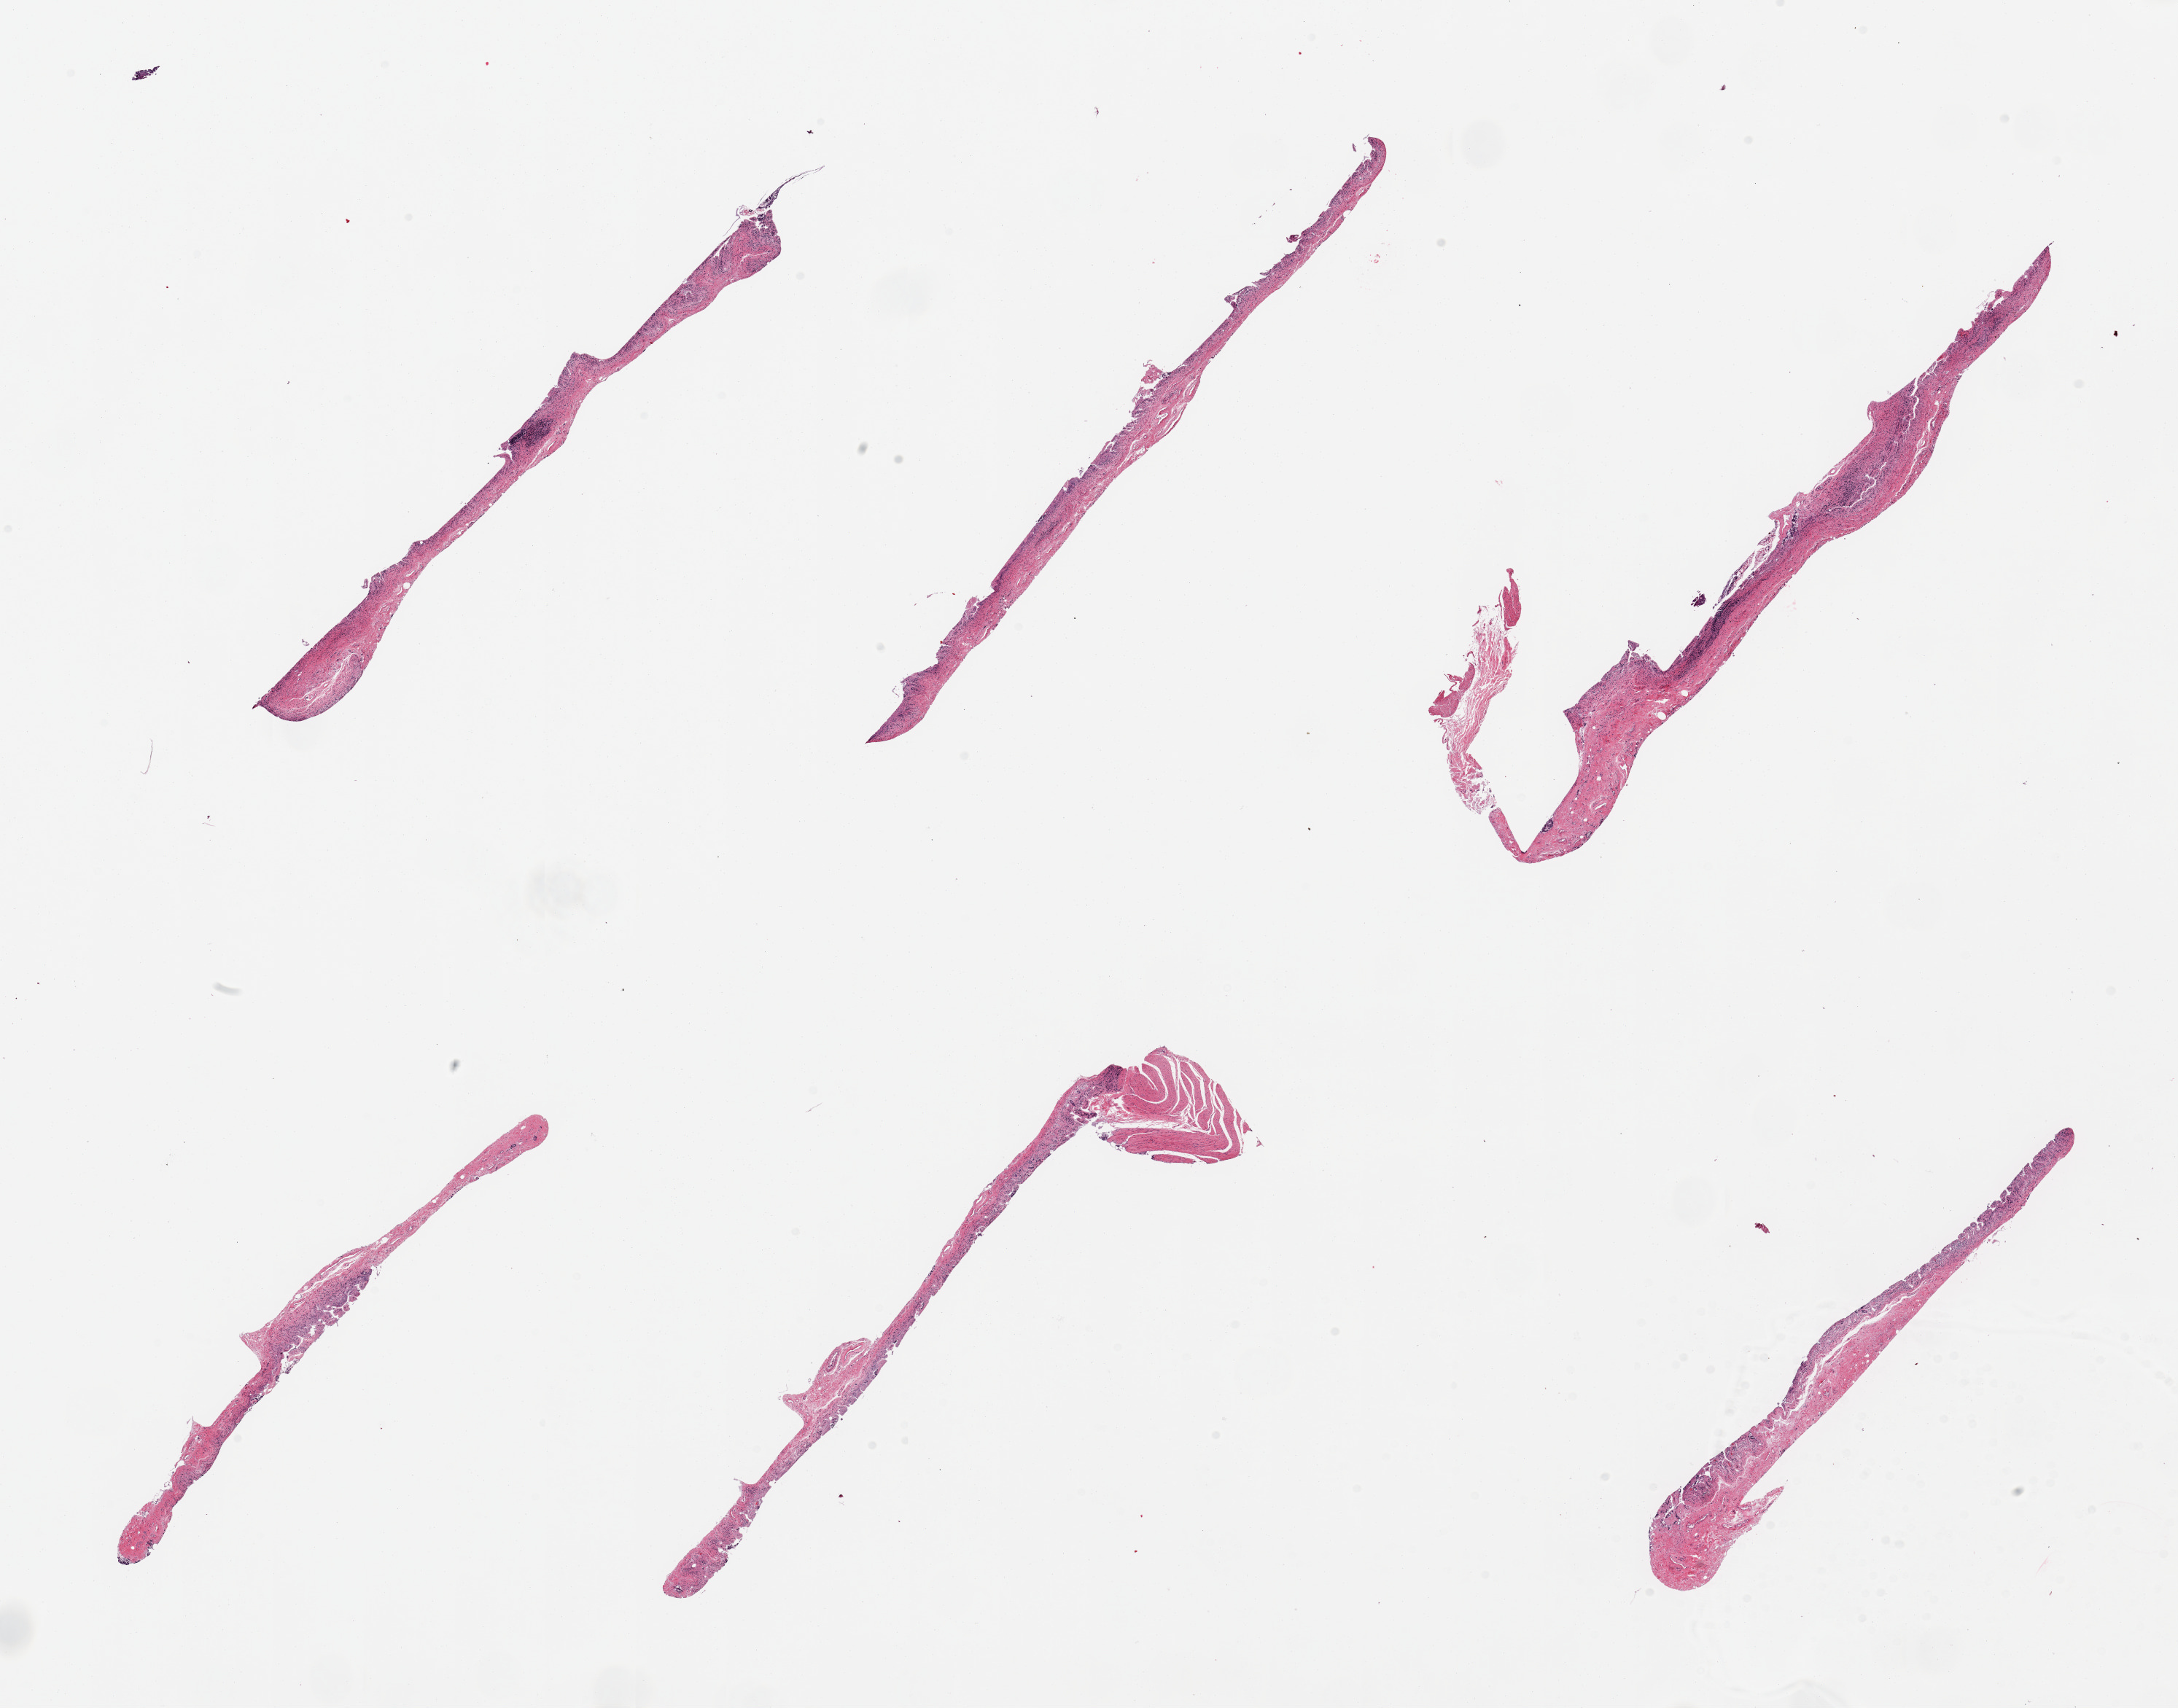
Whole-slide image, hematoxylin and eosin (H&E) stain, whole scanned area (about 23.6 x 18.5 mm, acquisition: 20x scan) shown as a low-resolution overview. PAXgene-fixed paraffin-embedded (PFPE) section. Target tissue: ileum. Tissue donor sample. Donor: male.
Pathologist's review note for this sample: 6 pieces, totally autolyzed, minimal residual lymphoid elements.